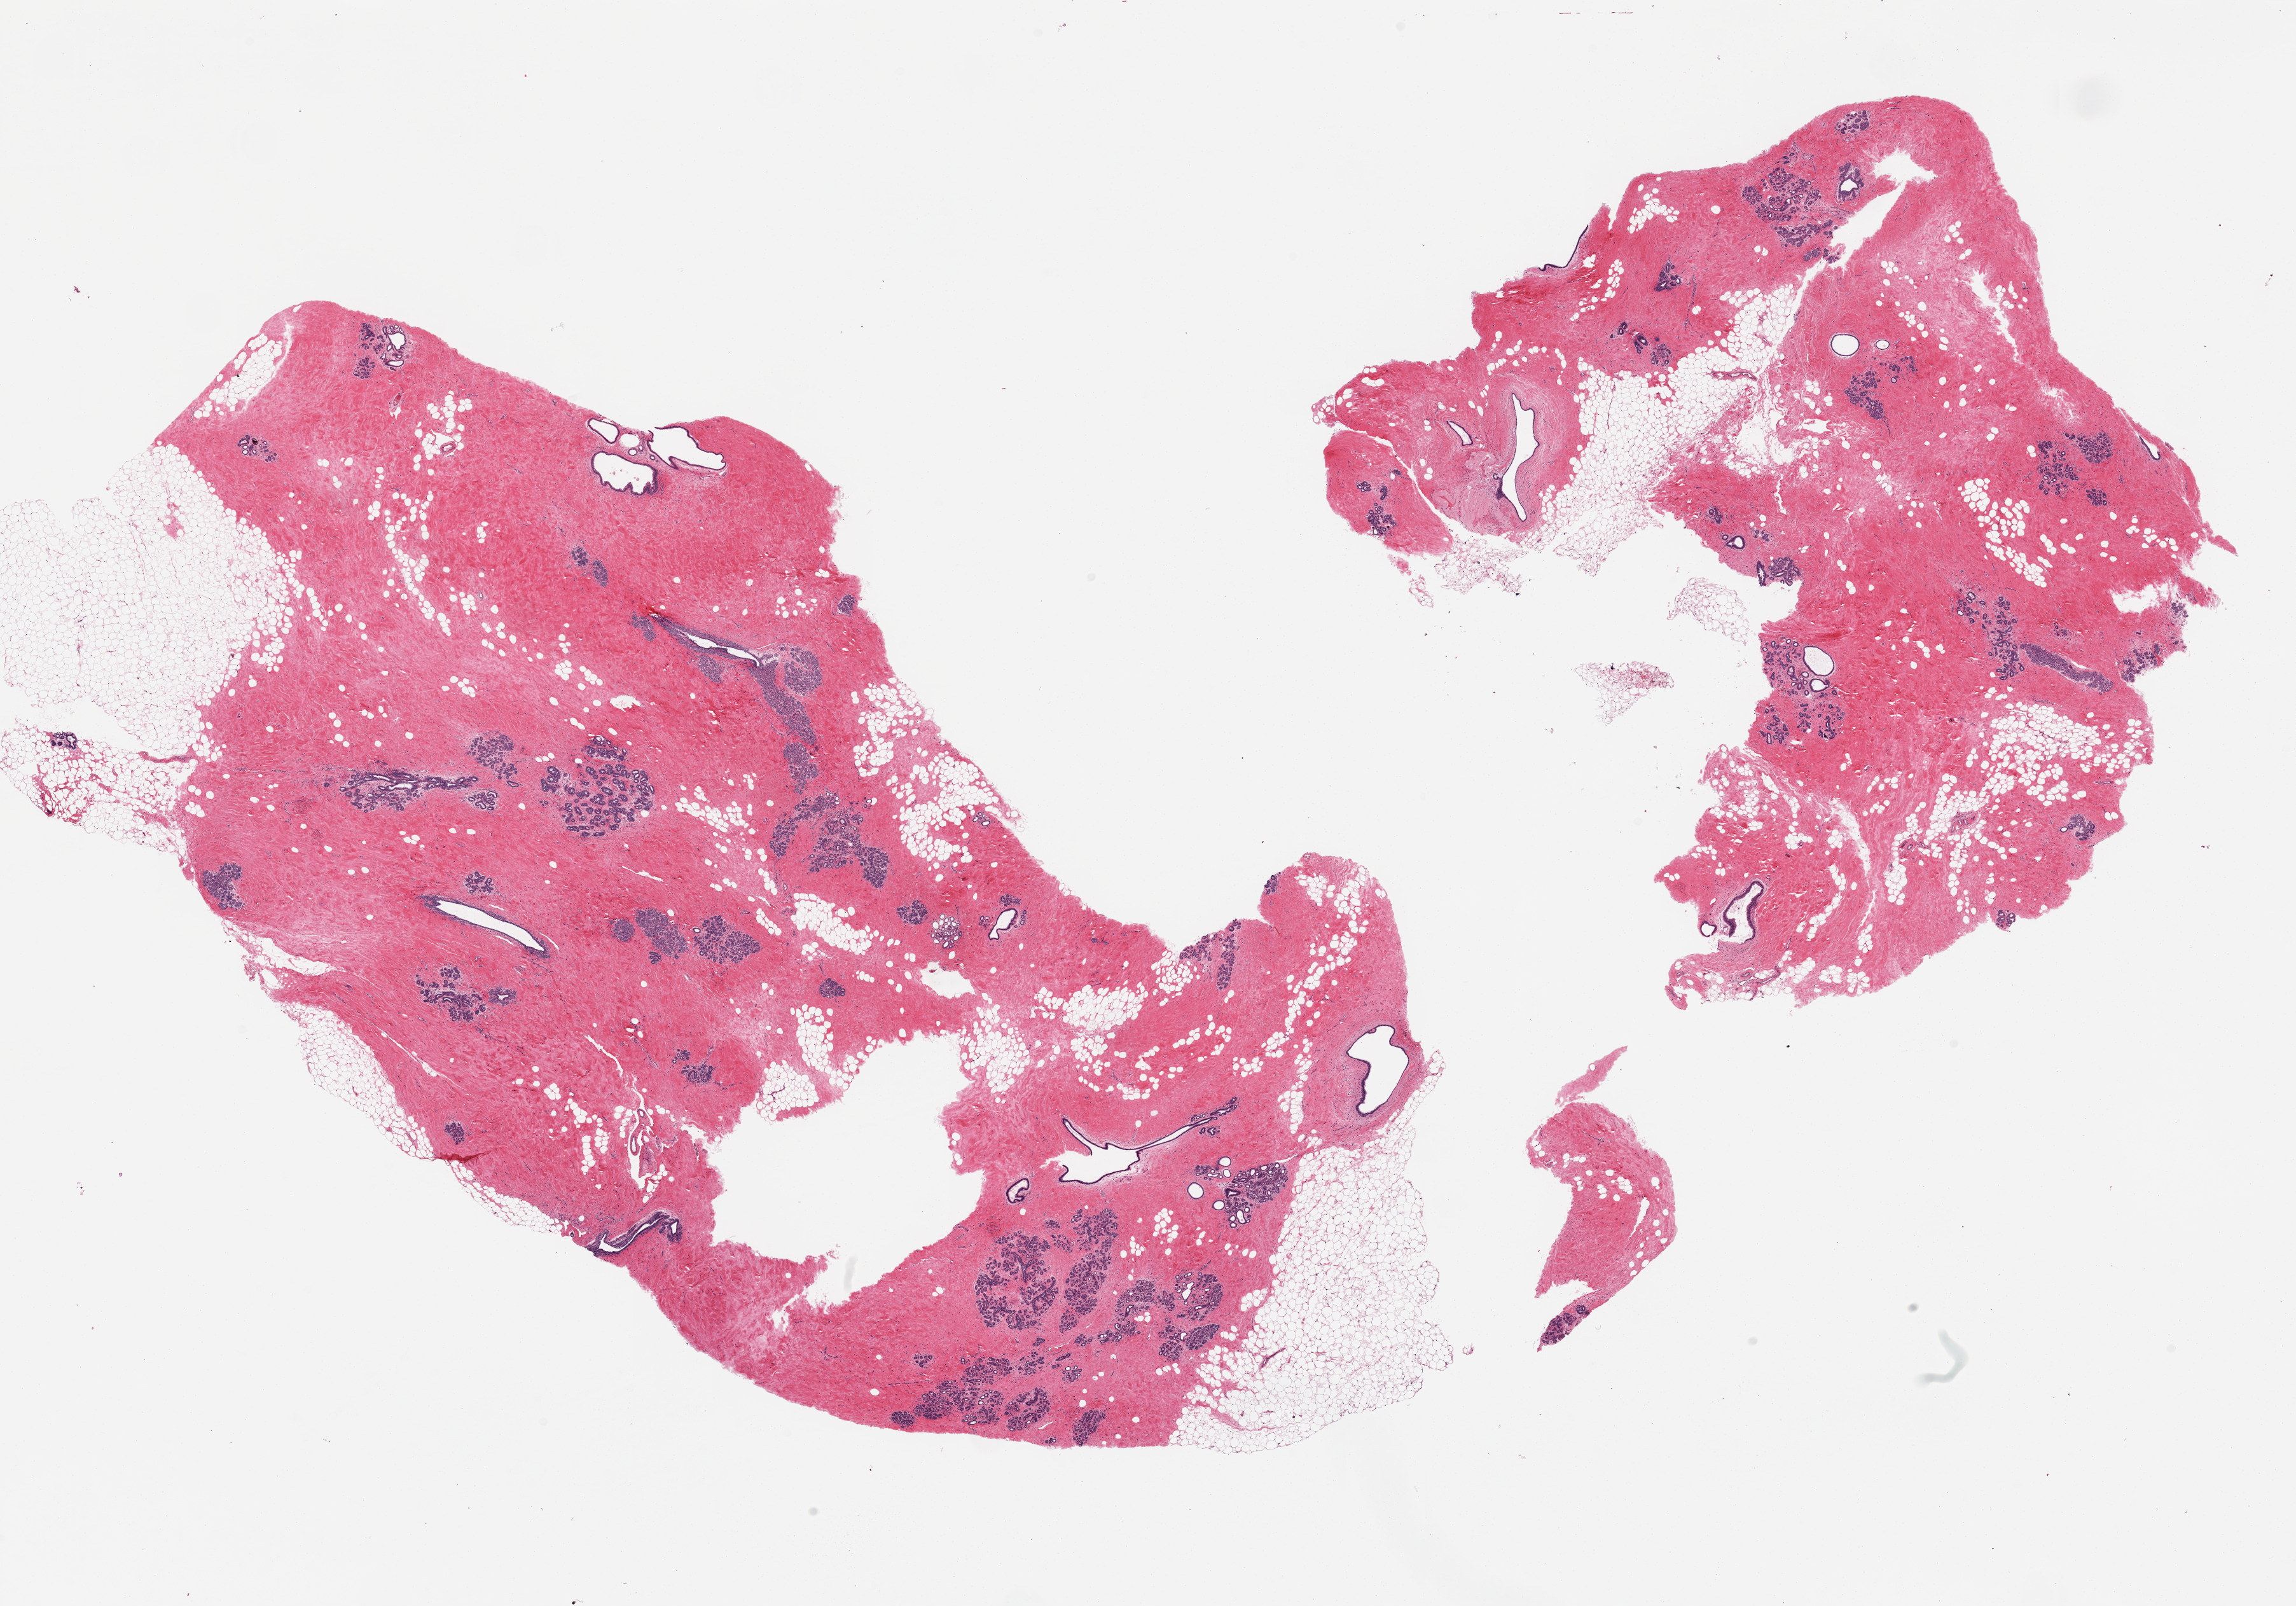
Digitized H&E-stained section — low-resolution overview of the scanned area, about 28.5 x 20.0 mm (slide scanned at 20x), PAXgene-fixed, paraffin-embedded tissue, sampled site (target tissue): breast, tissue donor sample. Female donor.
Reviewer comment on this tissue sample: 2 pieces. lobular neoplasia, grade 2 (atypical lobular hyperplasia).